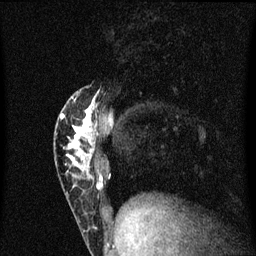
Breast MRI (dynamic contrast-enhanced), one sagittal slice. Position 19 of 60 along the scan axis. Dynamic contrast-enhanced series, image 2 of 3 at this slice position (ordered by acquisition). 1.5 T. TE 4.2 ms, TR 8.4 ms. 256 × 256 image matrix, field of view 200 × 200 mm. Female patient, age 40 years.
Outlined on this slice (semi-automatically segmented with operator editing):
- analysis volume of interest (the breast-tissue region the enhancement analysis was run in; not a lesion): box from (x=55, y=90) to (x=104, y=203) px
- tumour enhancement mask (voxels above the 70 % enhancement threshold inside the analysis volume of interest): (x=61, y=96)–(x=101, y=189)